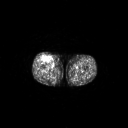
FDG PET of an extremity soft-tissue mass (from a PET/CT study), one axial slice. Slice 261 of 311 in the series (ordered by position). 3.27 mm slice thickness. 128 × 128 image matrix, field of view 700 × 700 mm. Male patient, age 56 years. Case-level facts recorded for this patient, not image findings: histological type: pleiomorphic leiomyosarcoma; grade: intermediate; site of the primary tumour: right thigh.
Annotated regions visible in this slice (expert contour drawn on MRI and transferred to this co-registered scan by the dataset authors):
- gross tumour volume including surrounding oedema: bounding box <41,55,51,62> (left, top, right, bottom; pixels)